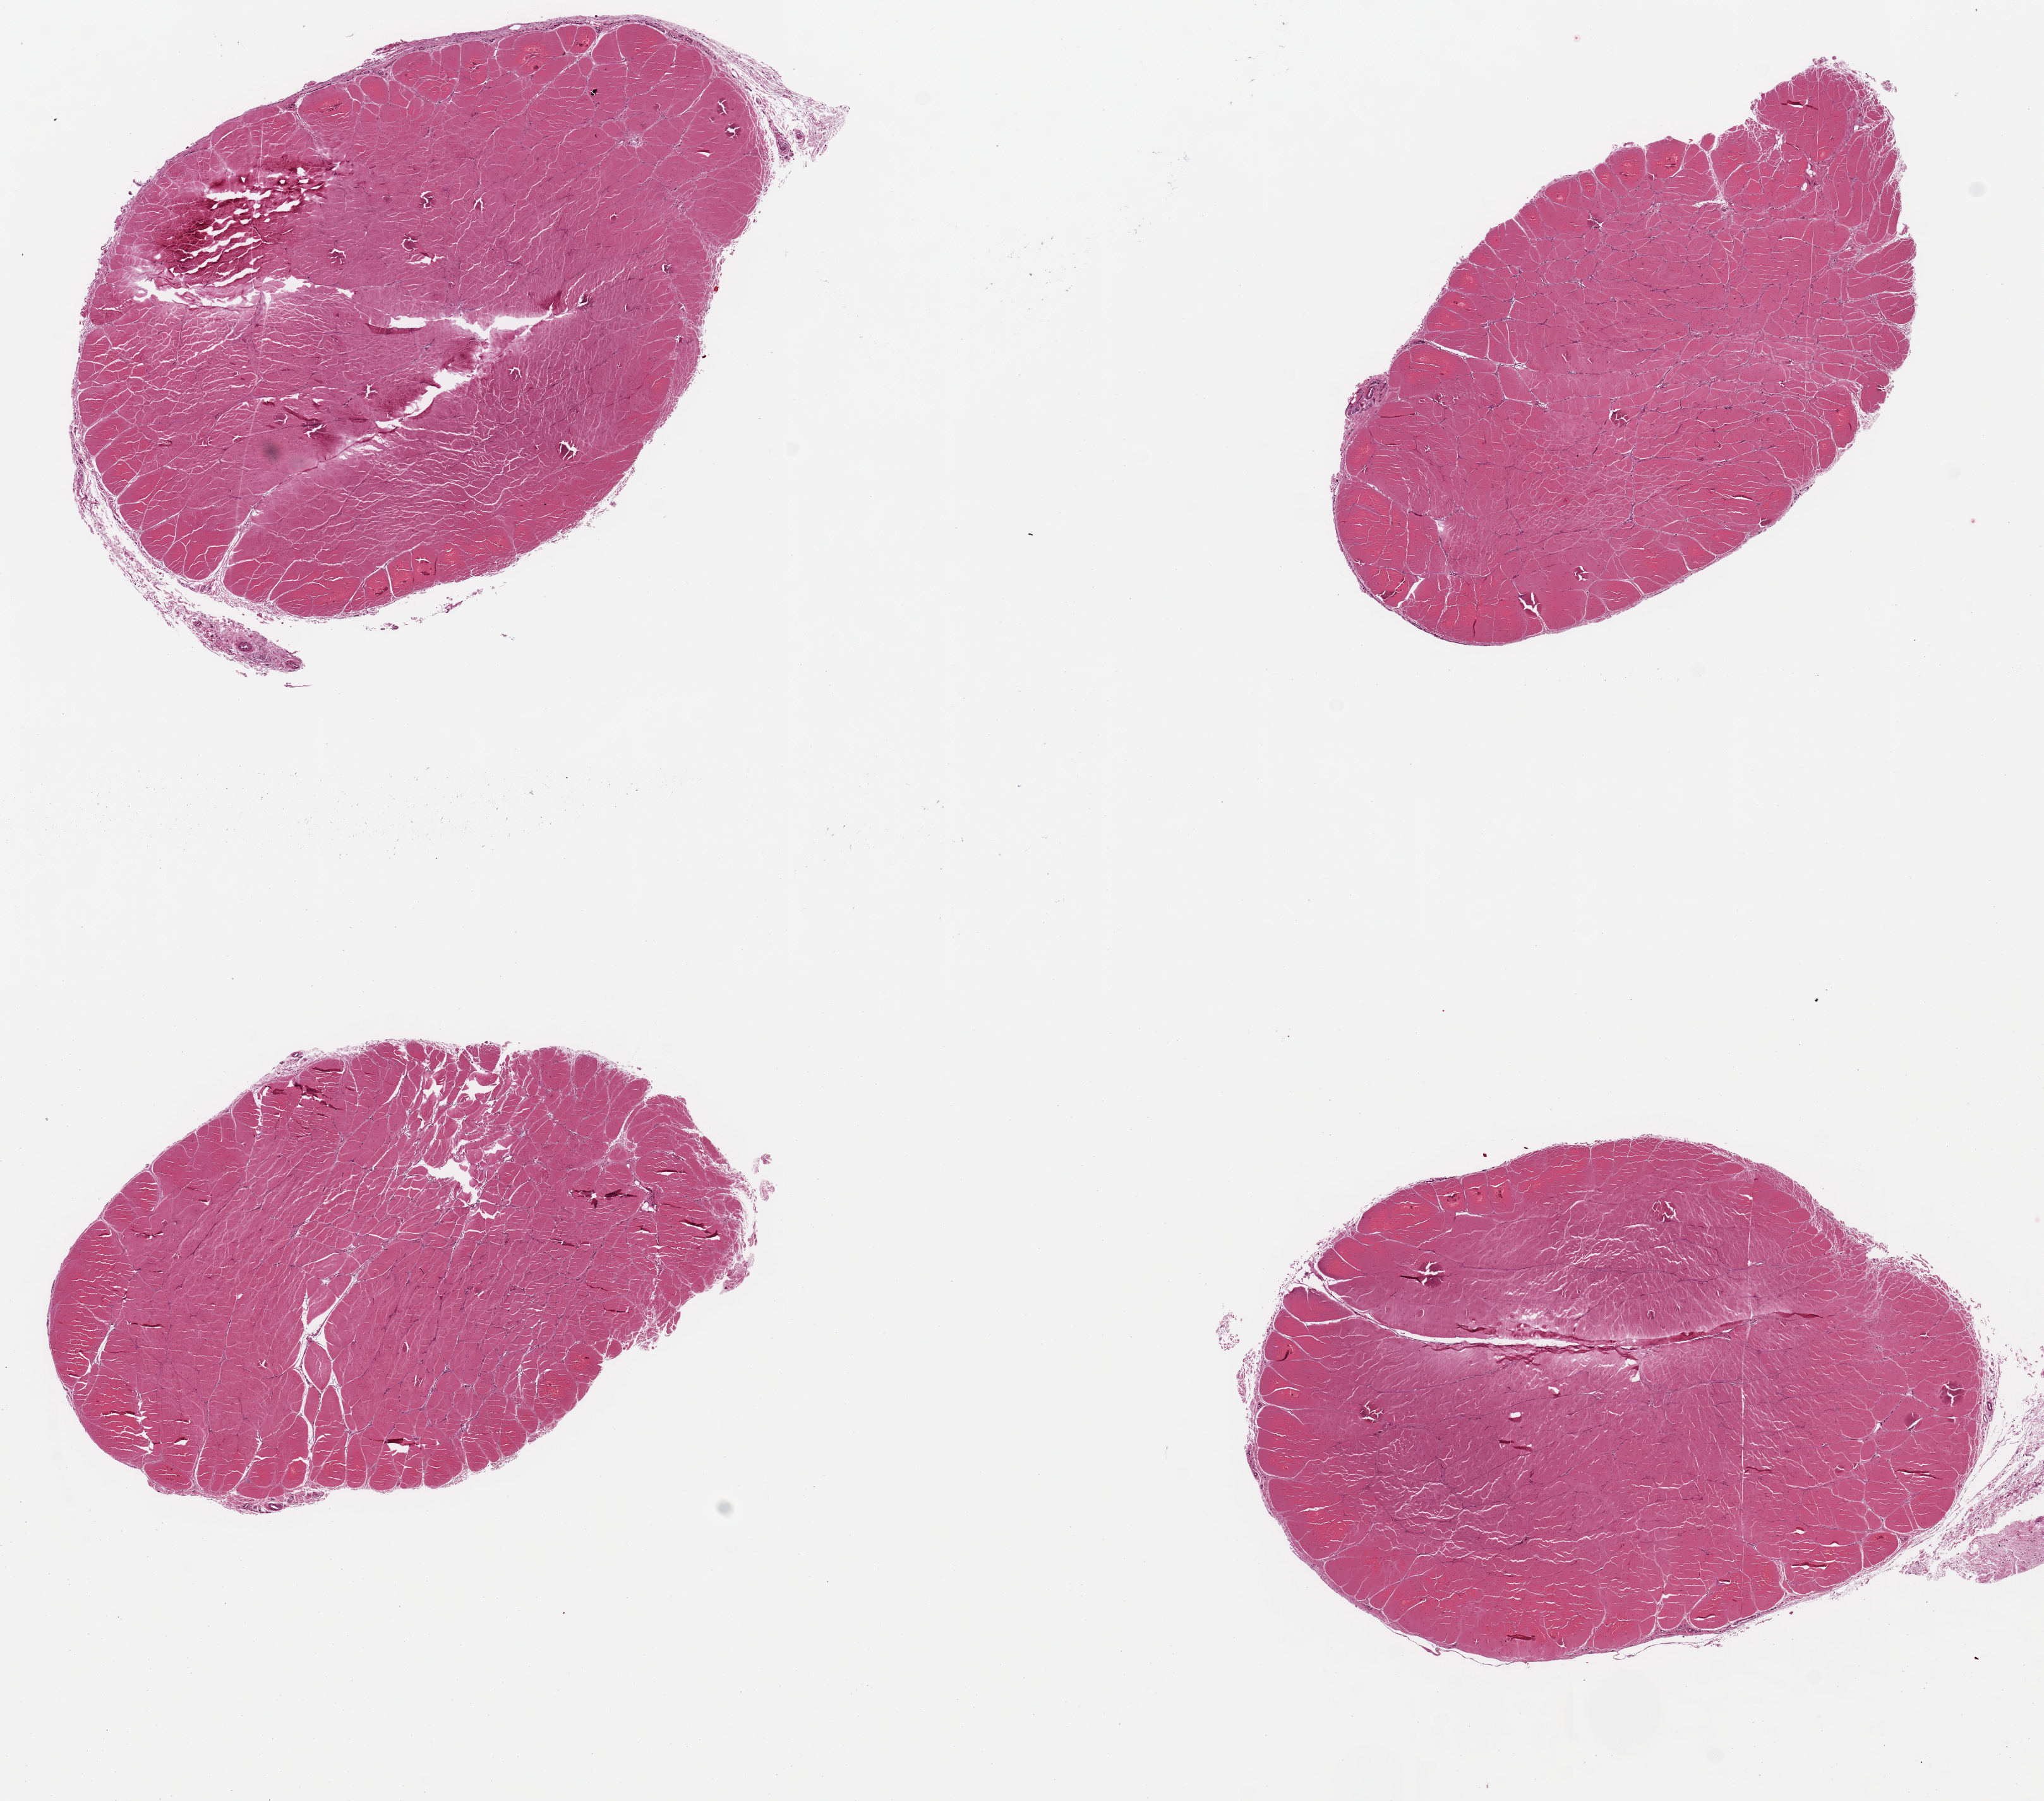
Whole-slide image, hematoxylin and eosin (H&E) stain, low-resolution overview of the scanned area, about 12.8 x 11.3 mm. Donor sex: female.
Specimen: PAXgene-fixed paraffin-embedded (PFPE) section; target tissue: tibial nerve; tissue donor sample.